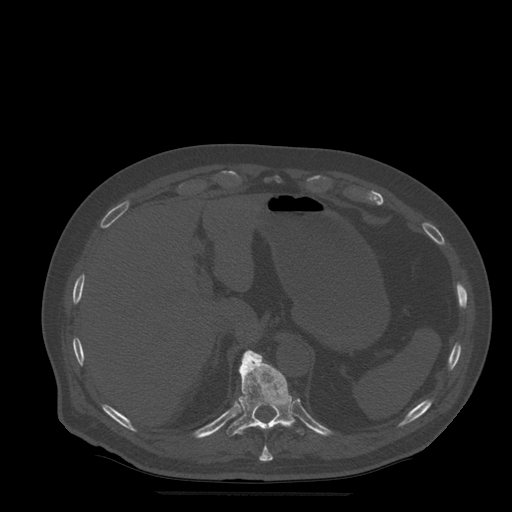
CT including the spine, one axial slice. Position 250 of 522 along the scan axis. Bone window (W 1800 / L 400 HU). 512 × 512 image matrix. Patient age 72 years. Case-level facts recorded for this patient, not image findings: primary cancer: prostate.
Annotated regions visible in this slice (semi-automatic segmentation, software-assisted and operator-edited):
- T10 vertebra: bounding box (x1, y1, x2, y2) in pixels: (260, 445, 273, 462)
- T11 vertebra: (227, 350, 305, 437)